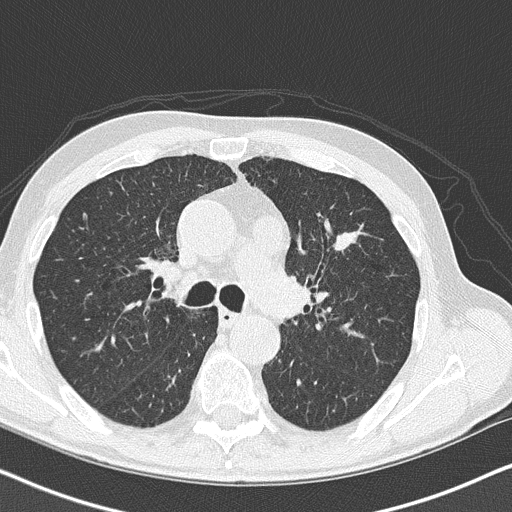
Chest CT (low-dose screening protocol), one axial image. Second annual screen. Lung window (W 1500 / L -600 HU). Slice 104 of 158 in the series. Male, age 73 years at enrolment. Current smoker at enrolment.
- Expert reader's lesion annotation, bounding box (x1, y1, x2, y2) in pixels: (312, 217, 375, 269).
- The screening reader recorded 3 non-calcified nodules or masses ≥4 mm on this exam; which of them this box marks is not recorded.
- Official screen result: positive, other.
- Participant outcome: lung cancer diagnosed 36 days after this screen — small cell carcinoma, NOS, left upper lobe, stage IIIB (AJCC 6th edition), 19 mm at pathology.